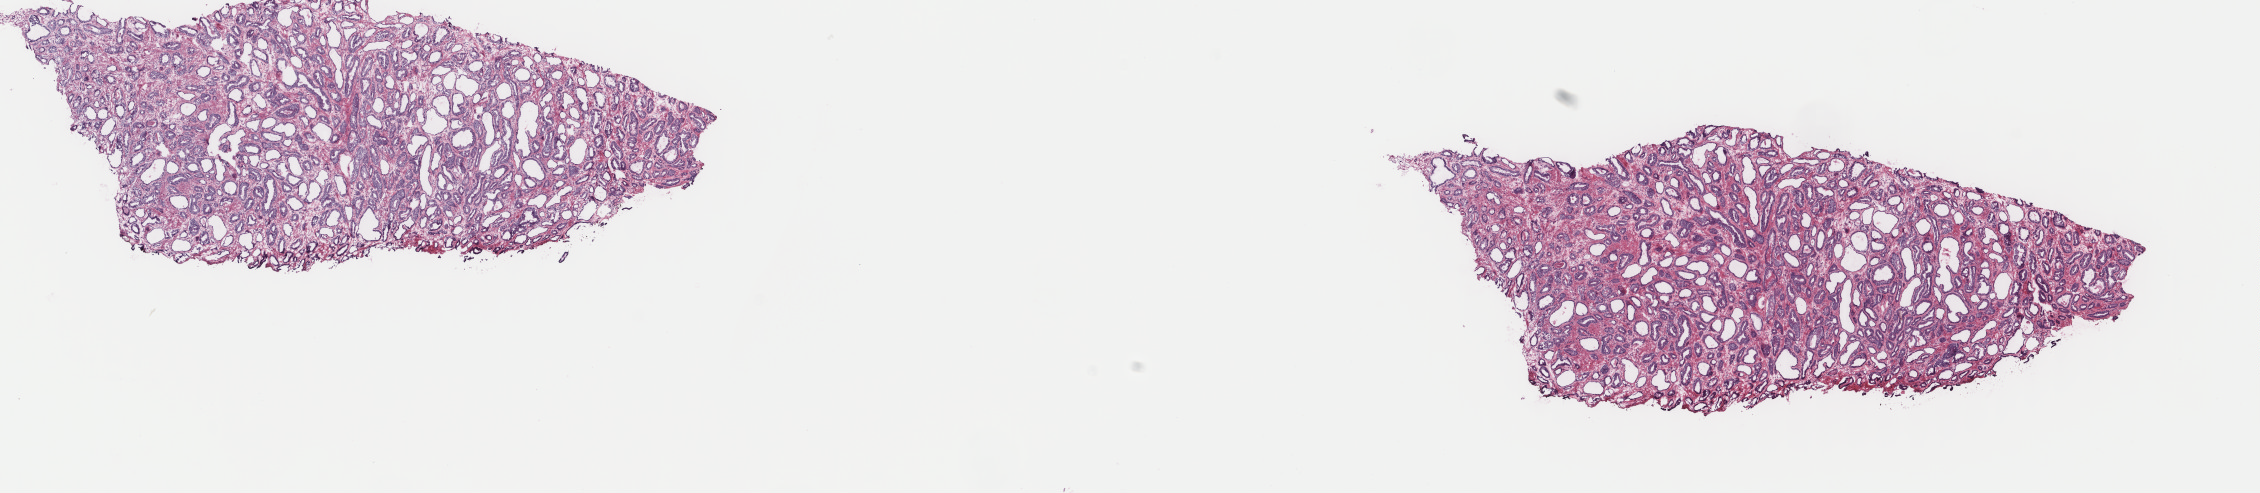
Hematoxylin and eosin (H&E) stained whole-slide image — a low-resolution overview of the entire scanned area, about 17.9 x 3.9 mm, frozen section from the top of the tissue portion, sample: primary tumour, prostate. Patient: male, age at initial diagnosis 62 years. Composition of this section per pathologist review: tumour cells 50%, tumour nuclei 60%.
Histologic diagnosis: Adenocarcinoma, NOS (prostate gland).